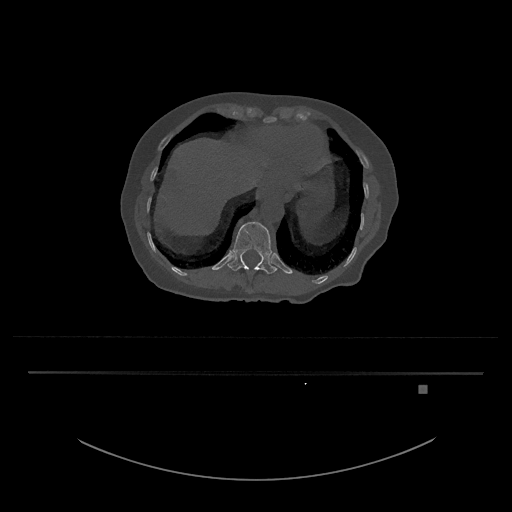
CT including the spine, one axial slice. Slice 621 of 797 in the series (ordered by position). Reconstruction kernel Br40s/3. 120 kVp. Bone window (W 1800 / L 400 HU). 0.5 mm slice thickness. 512 × 512 image matrix. Patient: female, 57 years. Case-level facts recorded for this patient, not image findings: primary cancer: cervical.
Outlined on this slice (semi-automatic segmentation, software-assisted and operator-edited):
- T12 vertebra: box from (x=227, y=222) to (x=278, y=274) px